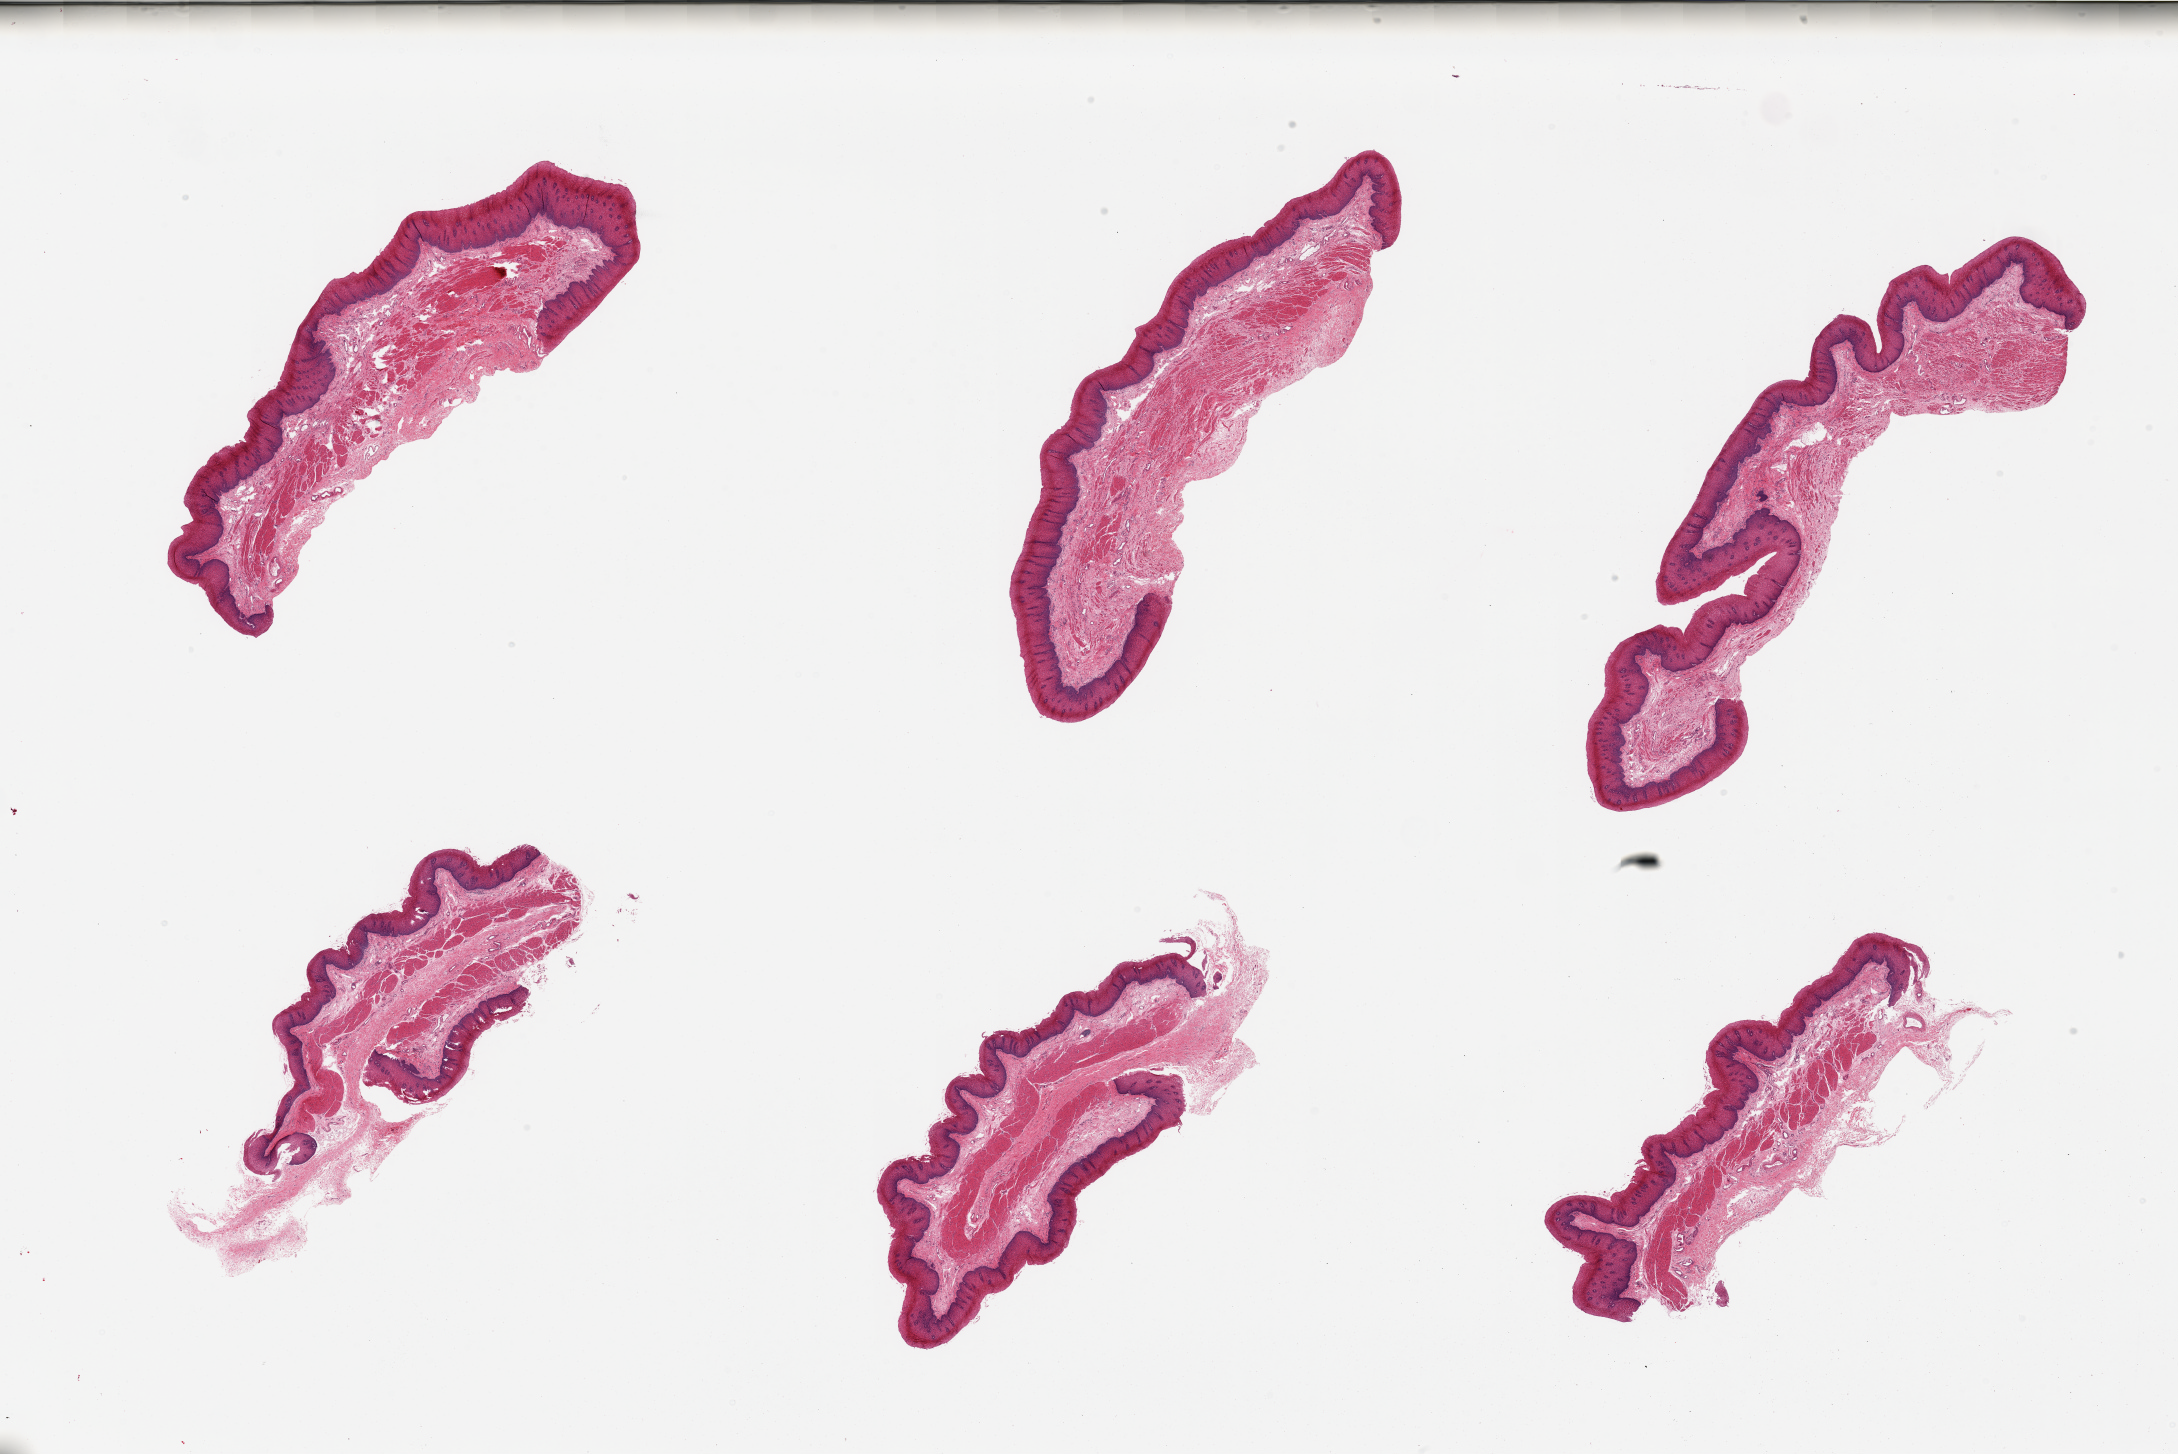
Digitized hematoxylin and eosin (H&E)-stained section, a low-resolution overview of the entire scanned area, about 34.5 x 23.0 mm. PAXgene-fixed, paraffin-embedded tissue. Section of esophageal mucous membrane (target tissue). Tissue donor sample. Donor sex: female.
Review note (as recorded): 6 pieces.